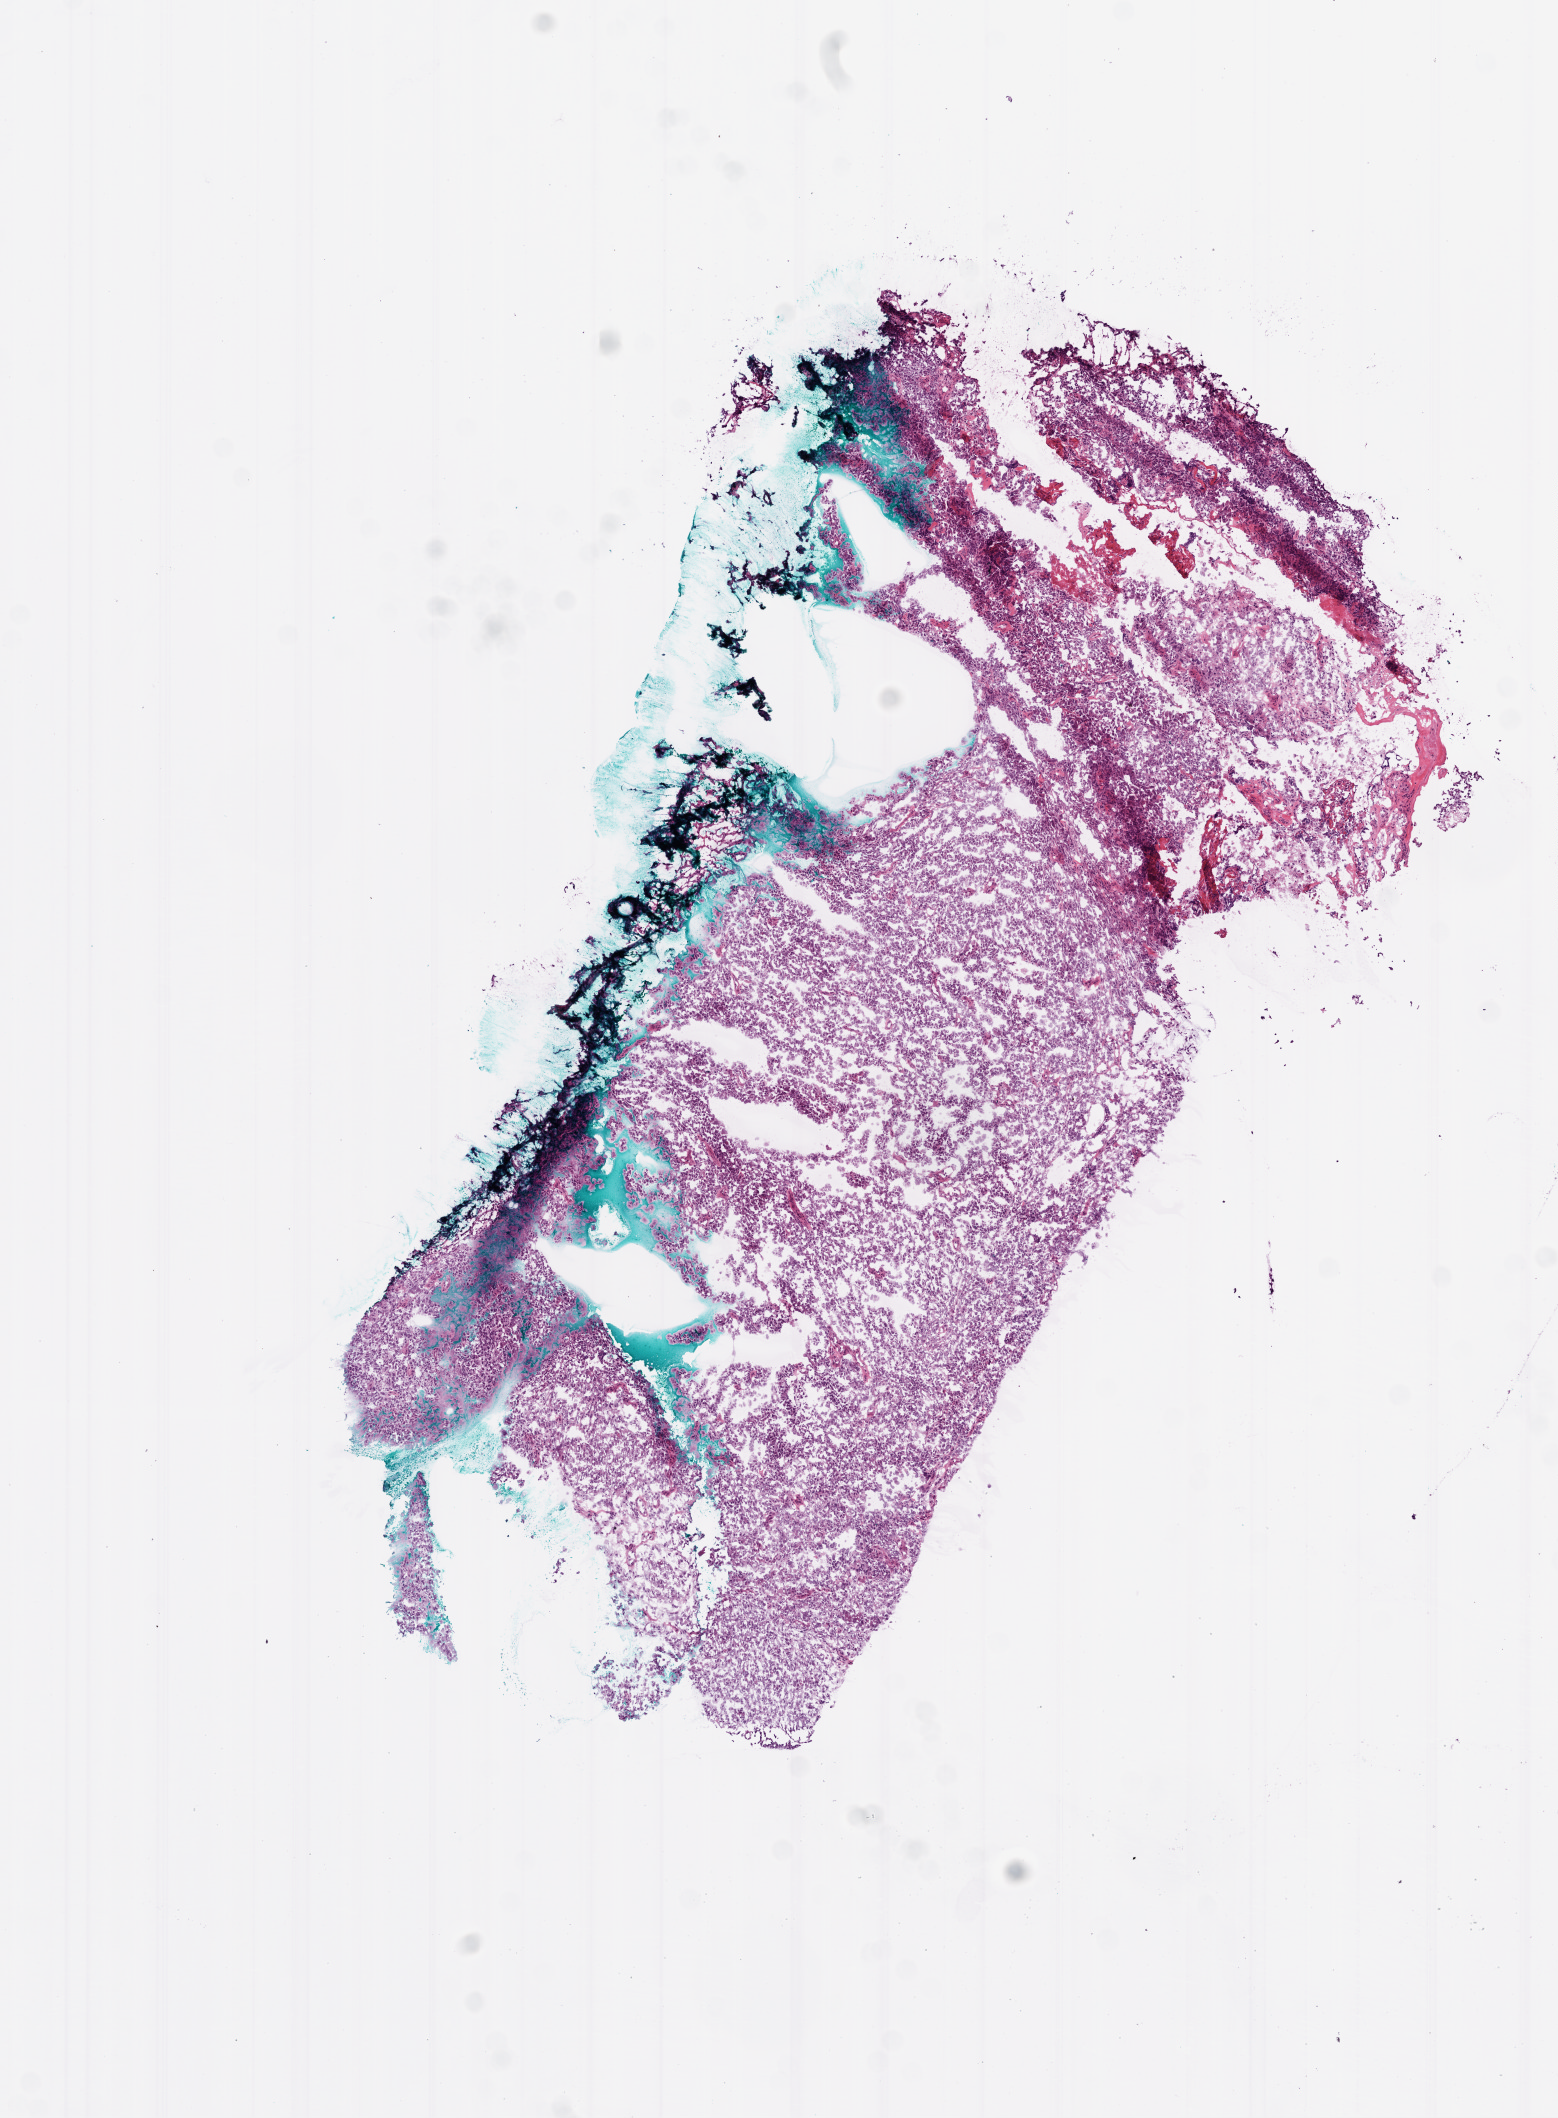
Whole-slide histology image, H&E-stained, a low-resolution overview of the entire scanned area, about 6.3 x 8.5 mm (from a 20x scan). Frozen section. Sample: primary tumour, ovary. Female, age 71 years at initial diagnosis. Histologic grade: G3 (poorly differentiated). Pathologist review of this section (percent, as recorded): tumour cells 90%, tumour nuclei 95%, normal cells 0%, stromal cells 5%, necrosis 5%. Infiltration values recorded for this section: lymphocyte infiltration 50%, neutrophil infiltration 50%.
- pathologic diagnosis: Serous cystadenocarcinoma, NOS
- FIGO stage: IIIC